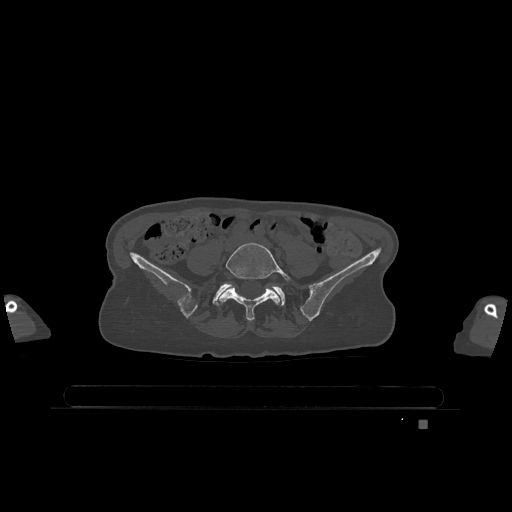
CT including the spine, one axial slice. Slice 232 of 1317 in the series (ordered by position). Bone window (W 1800 / L 400 HU). 512 × 512 image matrix. Patient: female, 74 years. From the clinical record (not read from this slice): primary cancer: lung.
Structures marked on this image (semi-automatic segmentation, software-assisted and operator-edited):
- L5 vertebra: bounding box <217,243,291,321> (left, top, right, bottom; pixels)